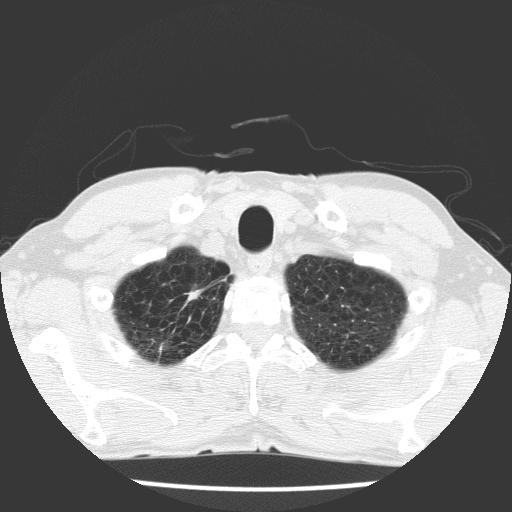
Axial slice from a low-dose chest CT screening exam; baseline screening round; lung window (W 1500 / L -600 HU); 2 mm slice thickness; slice 13 of 172 in the series; 512 × 512 image matrix. Male, age 63 years at enrolment. Current smoker at enrolment.
Lesion marked by an expert reader, bounding box <157,277,219,338> (left, top, right, bottom; pixels). No non-calcified nodule or mass ≥4 mm was recorded by the screening reader at this exam.